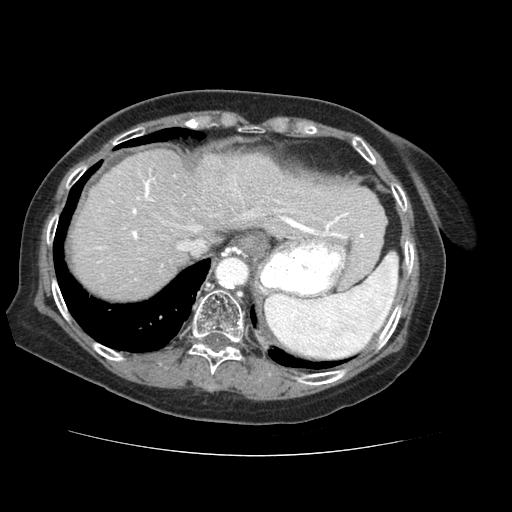
Contrast-enhanced abdominal CT (liver protocol), one axial slice. Slice 52 of 73 in the series (ordered by position). 120 kVp. Soft-tissue window (W 400 / L 40 HU). 512 × 512 image matrix, field of view 360 × 360 mm. Case-level facts recorded for this patient, not image findings: diagnosis: hepatocellular carcinoma (patient treated with transarterial chemoembolisation; whether this scan precedes or follows treatment is not stated here); TNM stage (as recorded): Stage-IVB; Child-Pugh class: A; tumour nodularity: uninodular.
Outlined on this slice (semi-automatic segmentation, software-assisted and operator-edited):
- abdominal aorta: bounding box [x1, y1, x2, y2] px = [217, 259, 248, 286]
- liver parenchyma outside the tumour (the mass and vessels are separate outlines, so this box may not span the whole liver): [72, 150, 380, 298]
- liver vessels: [97, 169, 347, 263]